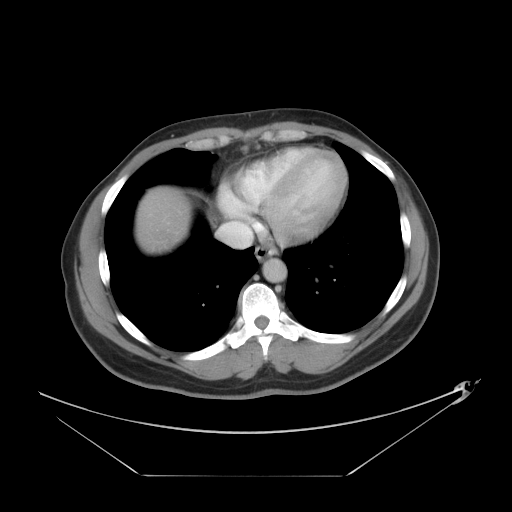
Contrast-enhanced abdominal CT, one axial slice; position 40 of 44 along the scan axis; reconstruction kernel STANDARD; 120 kVp; intravenous contrast given; soft-tissue window (W 400 / L 40 HU); 5 mm slice thickness; 512 × 512 image matrix, field of view 466 × 466 mm. Male patient, age 49 years. From the clinical record (not read from this slice): diagnosis: colorectal cancer liver metastases, imaged before liver resection; multiple liver metastases: no; largest metastasis: 8.5 cm; disease in both lobes: yes.
Outlined on this slice (expert manual segmentation):
- liver: bounding box <134,184,196,256> (left, top, right, bottom; pixels)